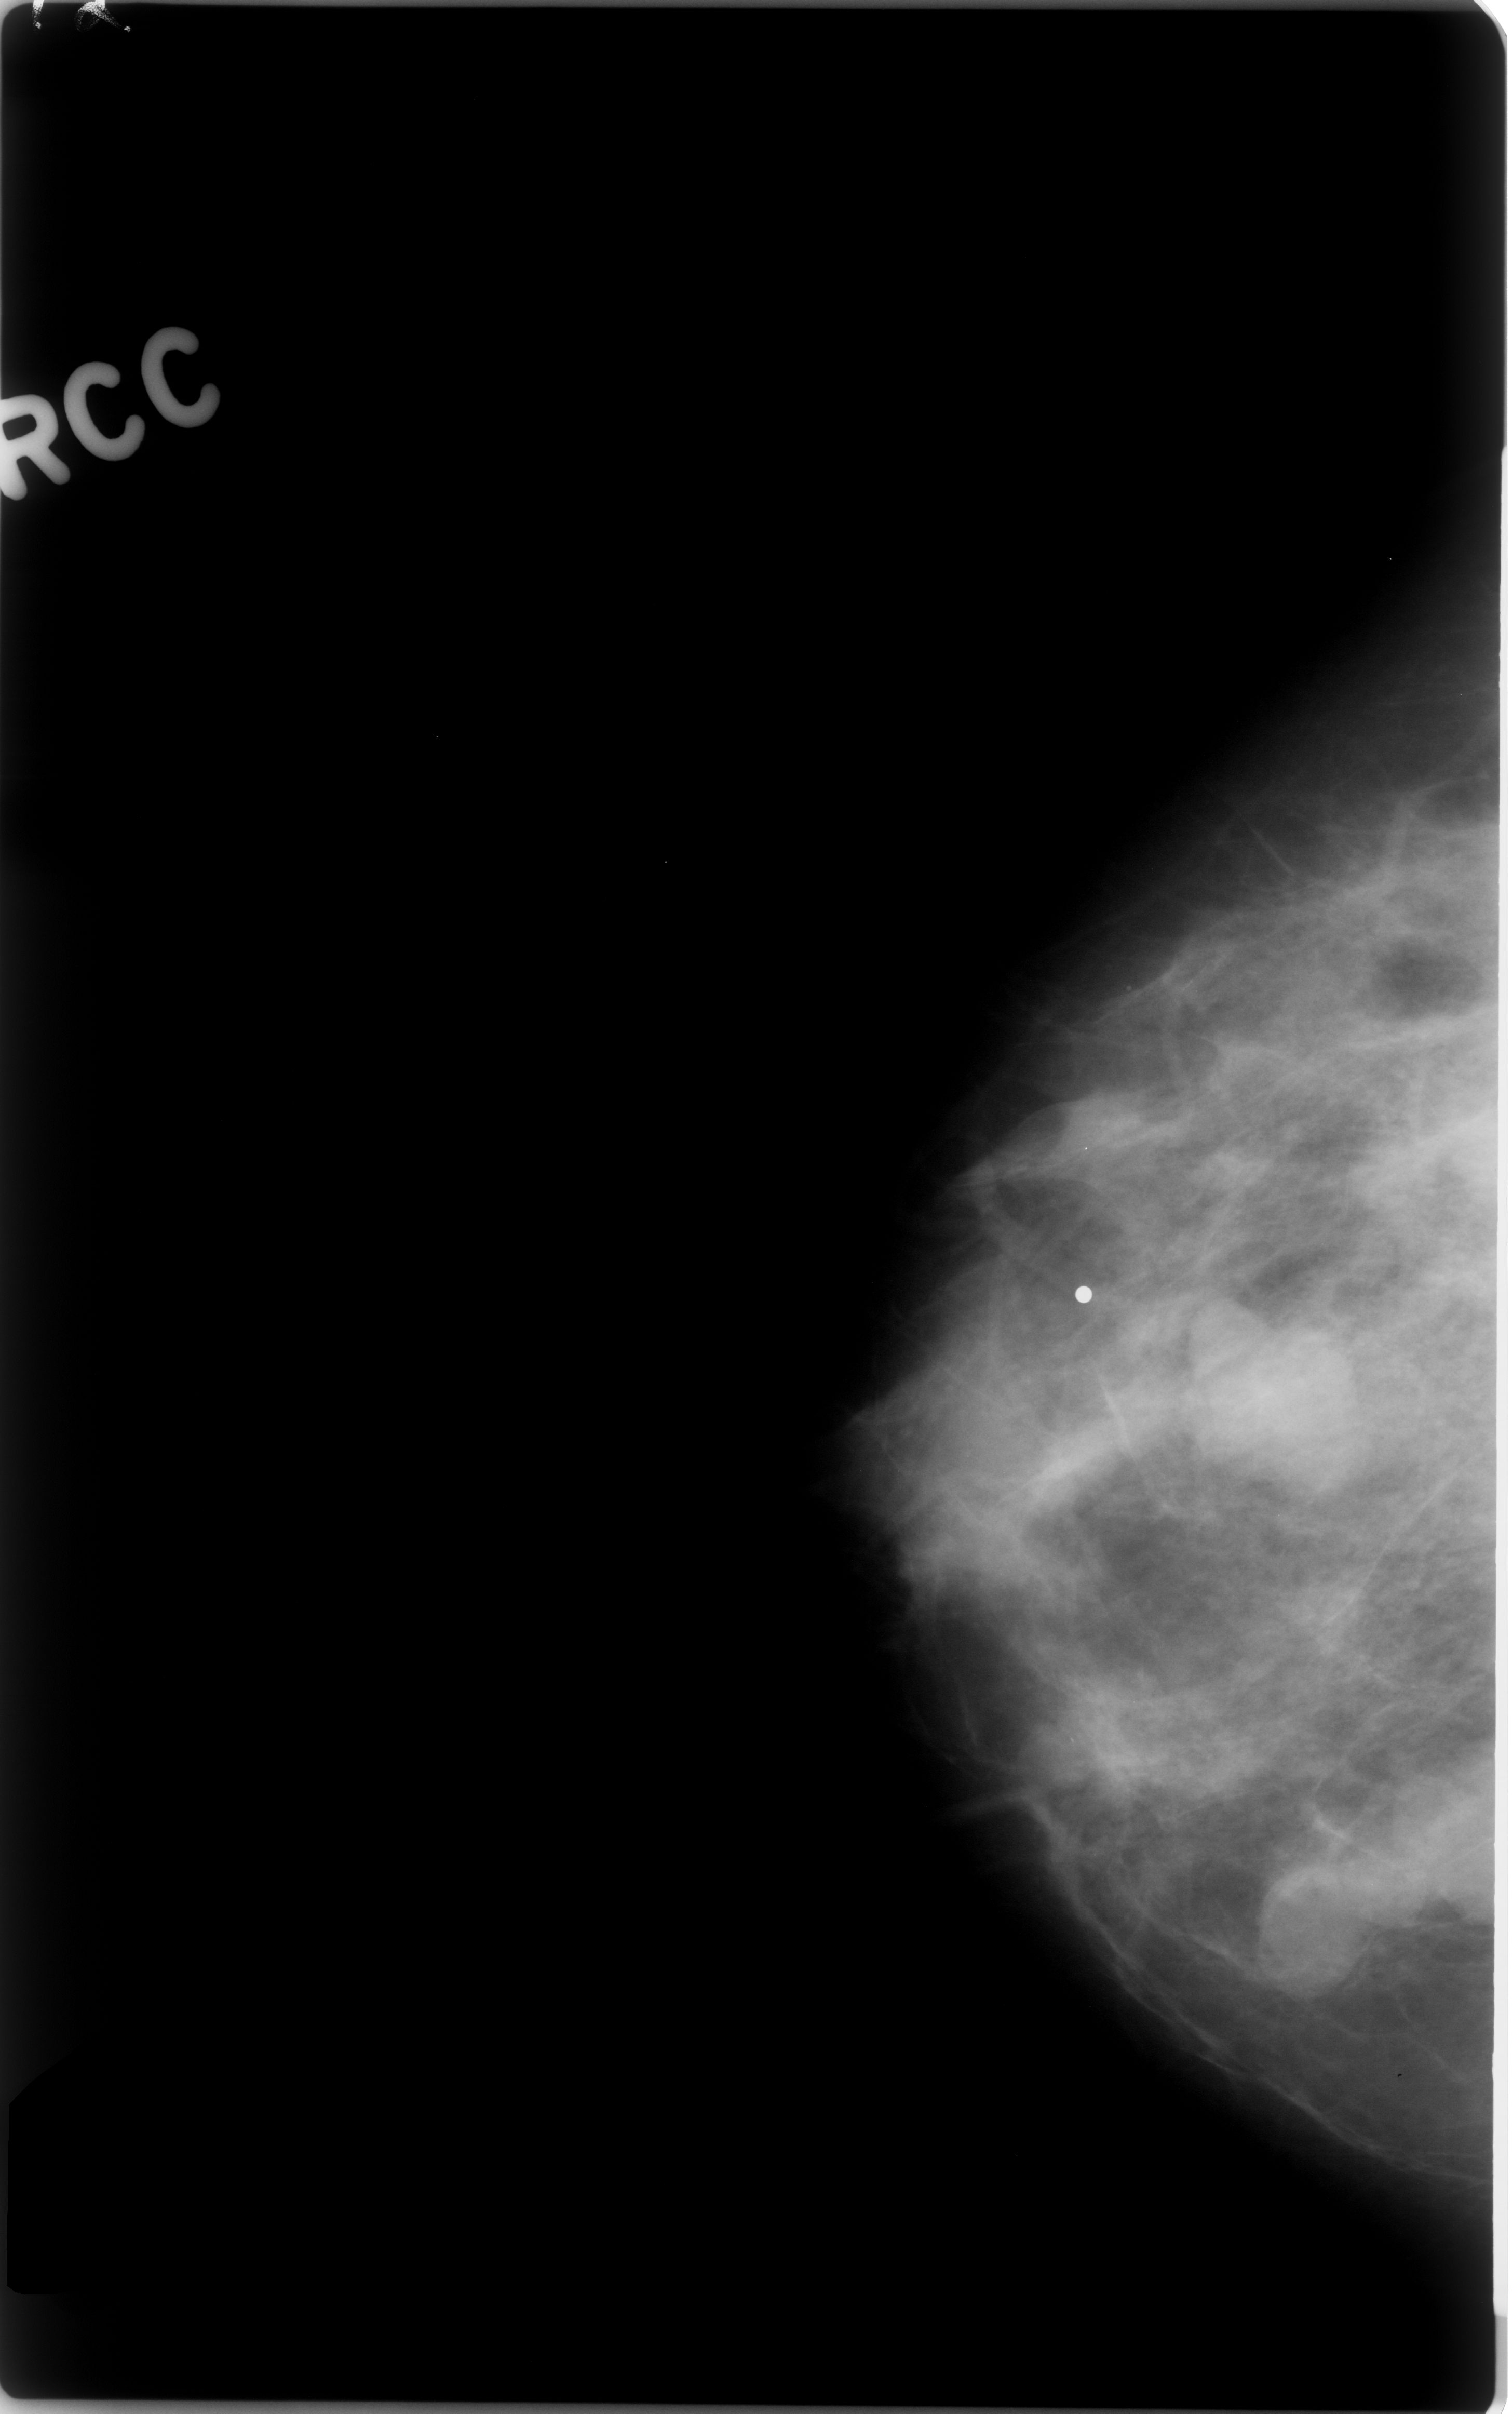
Scanned film-screen mammogram. Right breast. Craniocaudal (CC) view. BI-RADS breast density category 3 (scale 1–4). 1512 × 2414 image matrix.
Expert-marked regions of interest on this image (one box per marked abnormality):
- mass, shape lobulated, margins circumscribed; BI-RADS assessment category 4; subtlety rating 5 on a 1 (subtle) to 5 (obvious) scale; pathology (as recorded): benign: bounding box (x1, y1, x2, y2) in pixels: (1162, 1274, 1372, 1500)